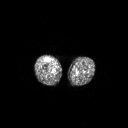
FDG PET of an extremity soft-tissue mass (from a PET/CT study), one axial slice; 128 × 128 image matrix, field of view 700 × 700 mm. Patient: male, 56 years. From the clinical record (not read from this slice): histological type: pleiomorphic leiomyosarcoma; grade: intermediate; site of the primary tumour: right thigh.
Structures marked on this image (expert contour drawn on MRI and transferred to this co-registered scan by the dataset authors):
- gross tumour volume including surrounding oedema: bounding box (x1, y1, x2, y2) in pixels: (45, 57, 51, 62)